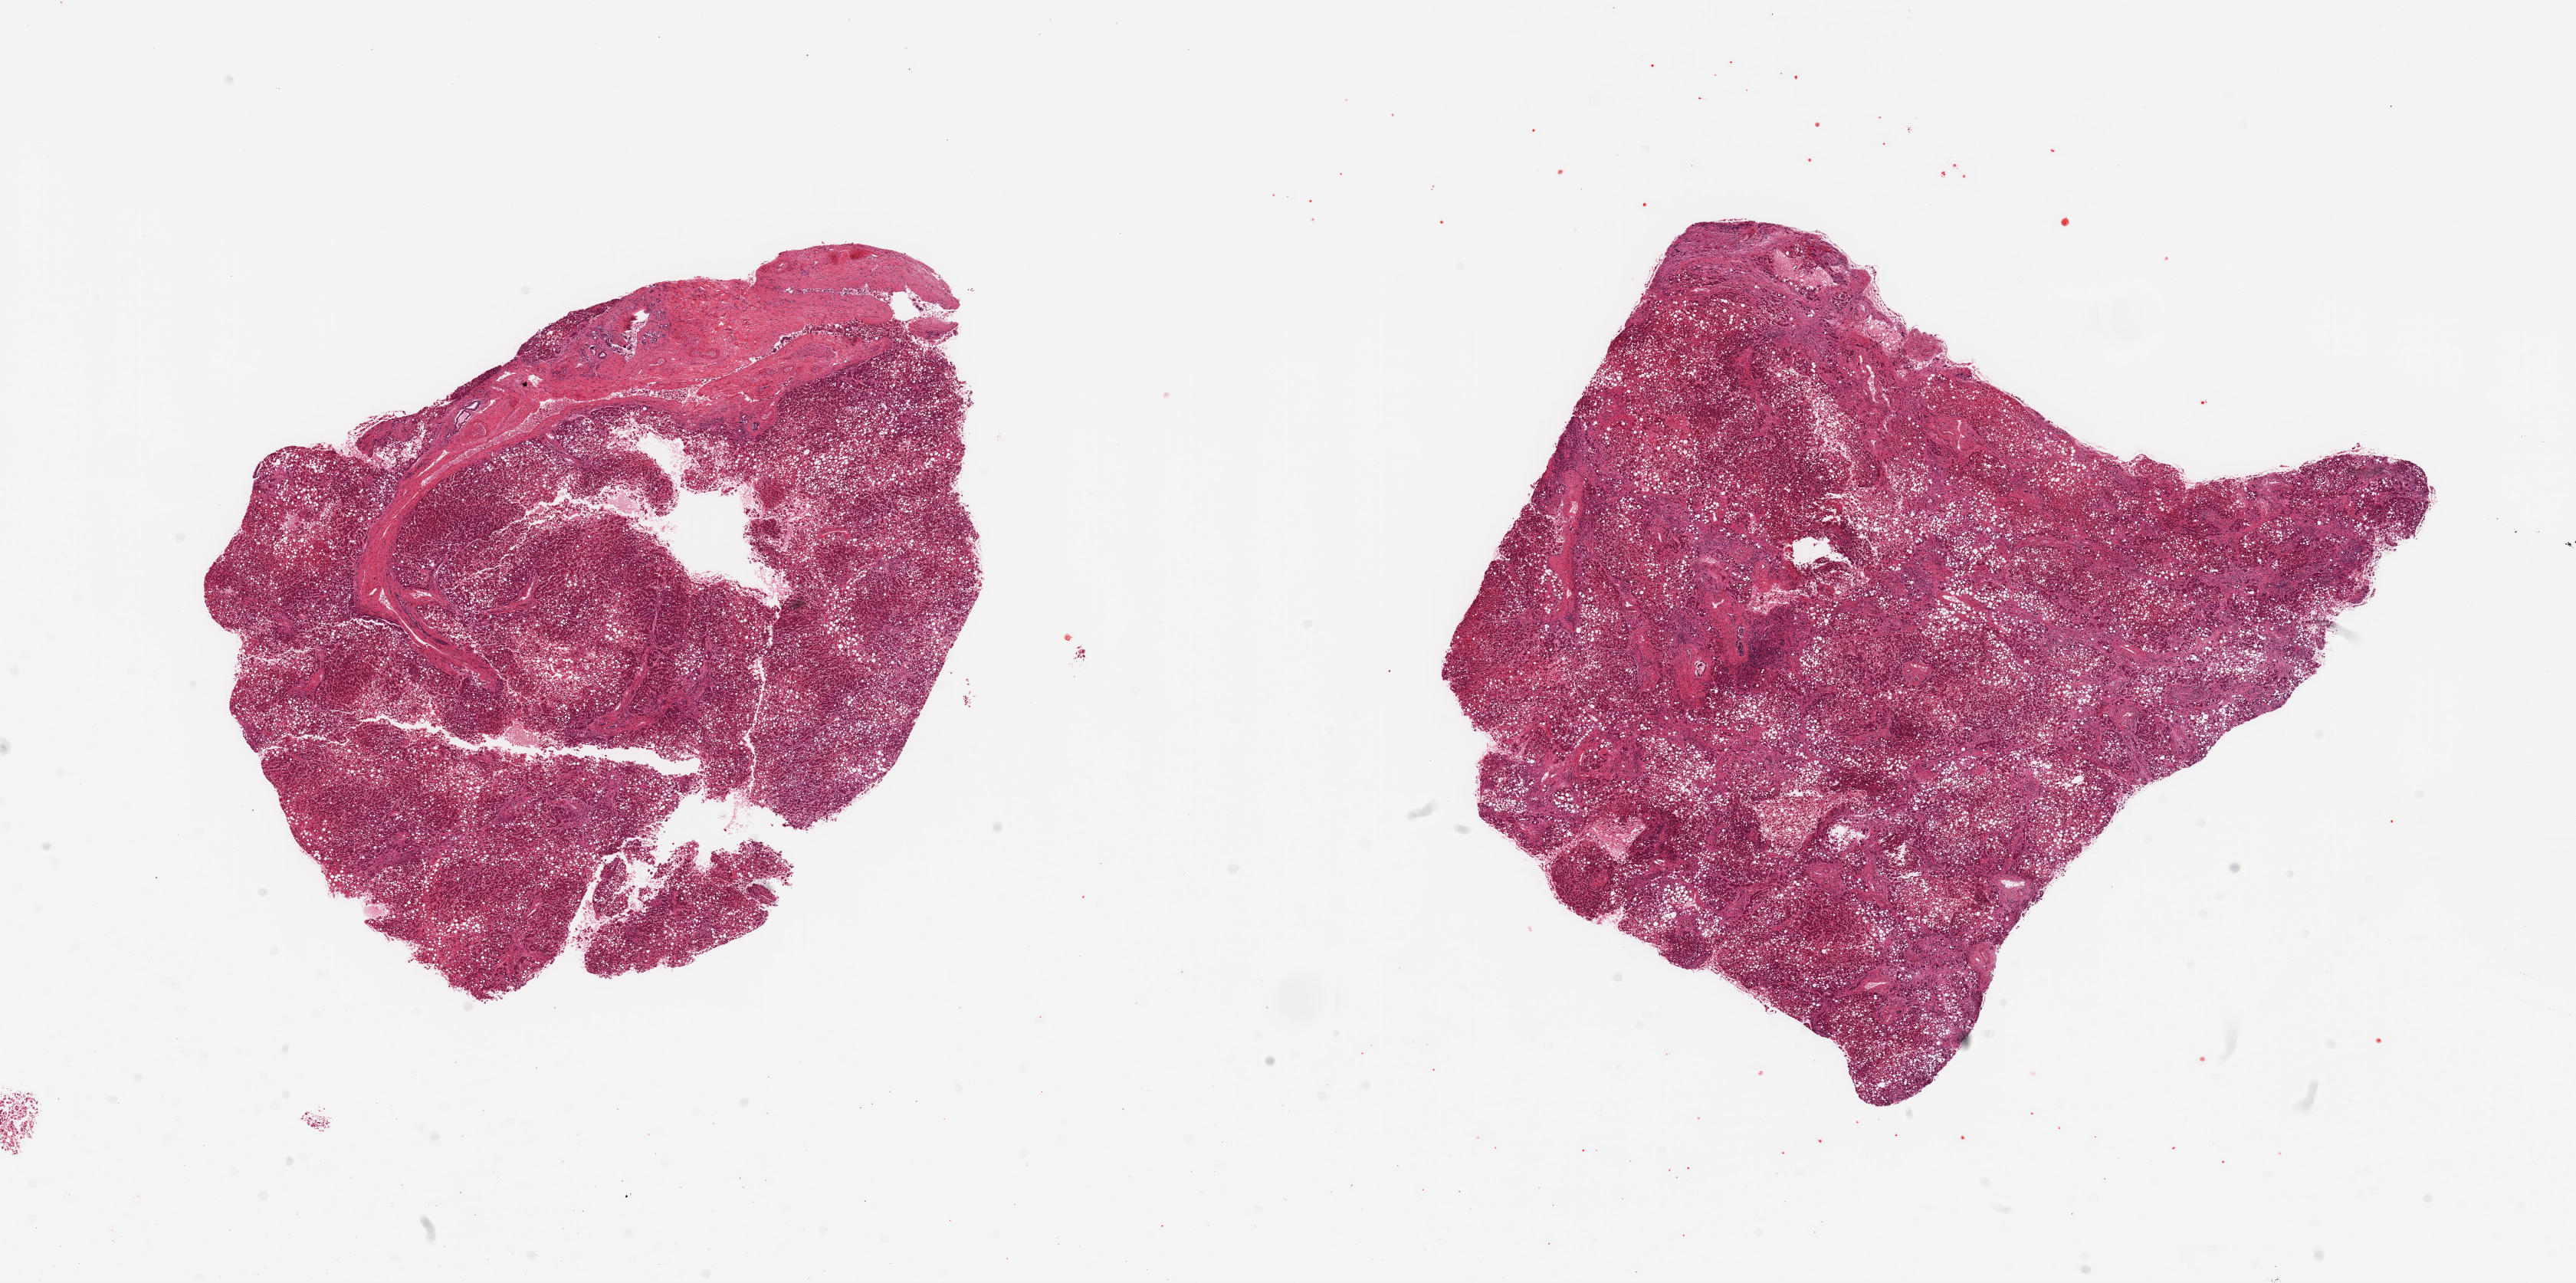
H&E whole-slide image — a low-resolution overview of the entire scanned area, about 26.6 x 13.2 mm; PAXgene-fixed, paraffin-embedded tissue; sampled site (target tissue): liver; donor tissue sample. Donor sex: female.
- review note (as recorded): 2 pieces; severe macrovesicular steatosis (80%) & fibrosis